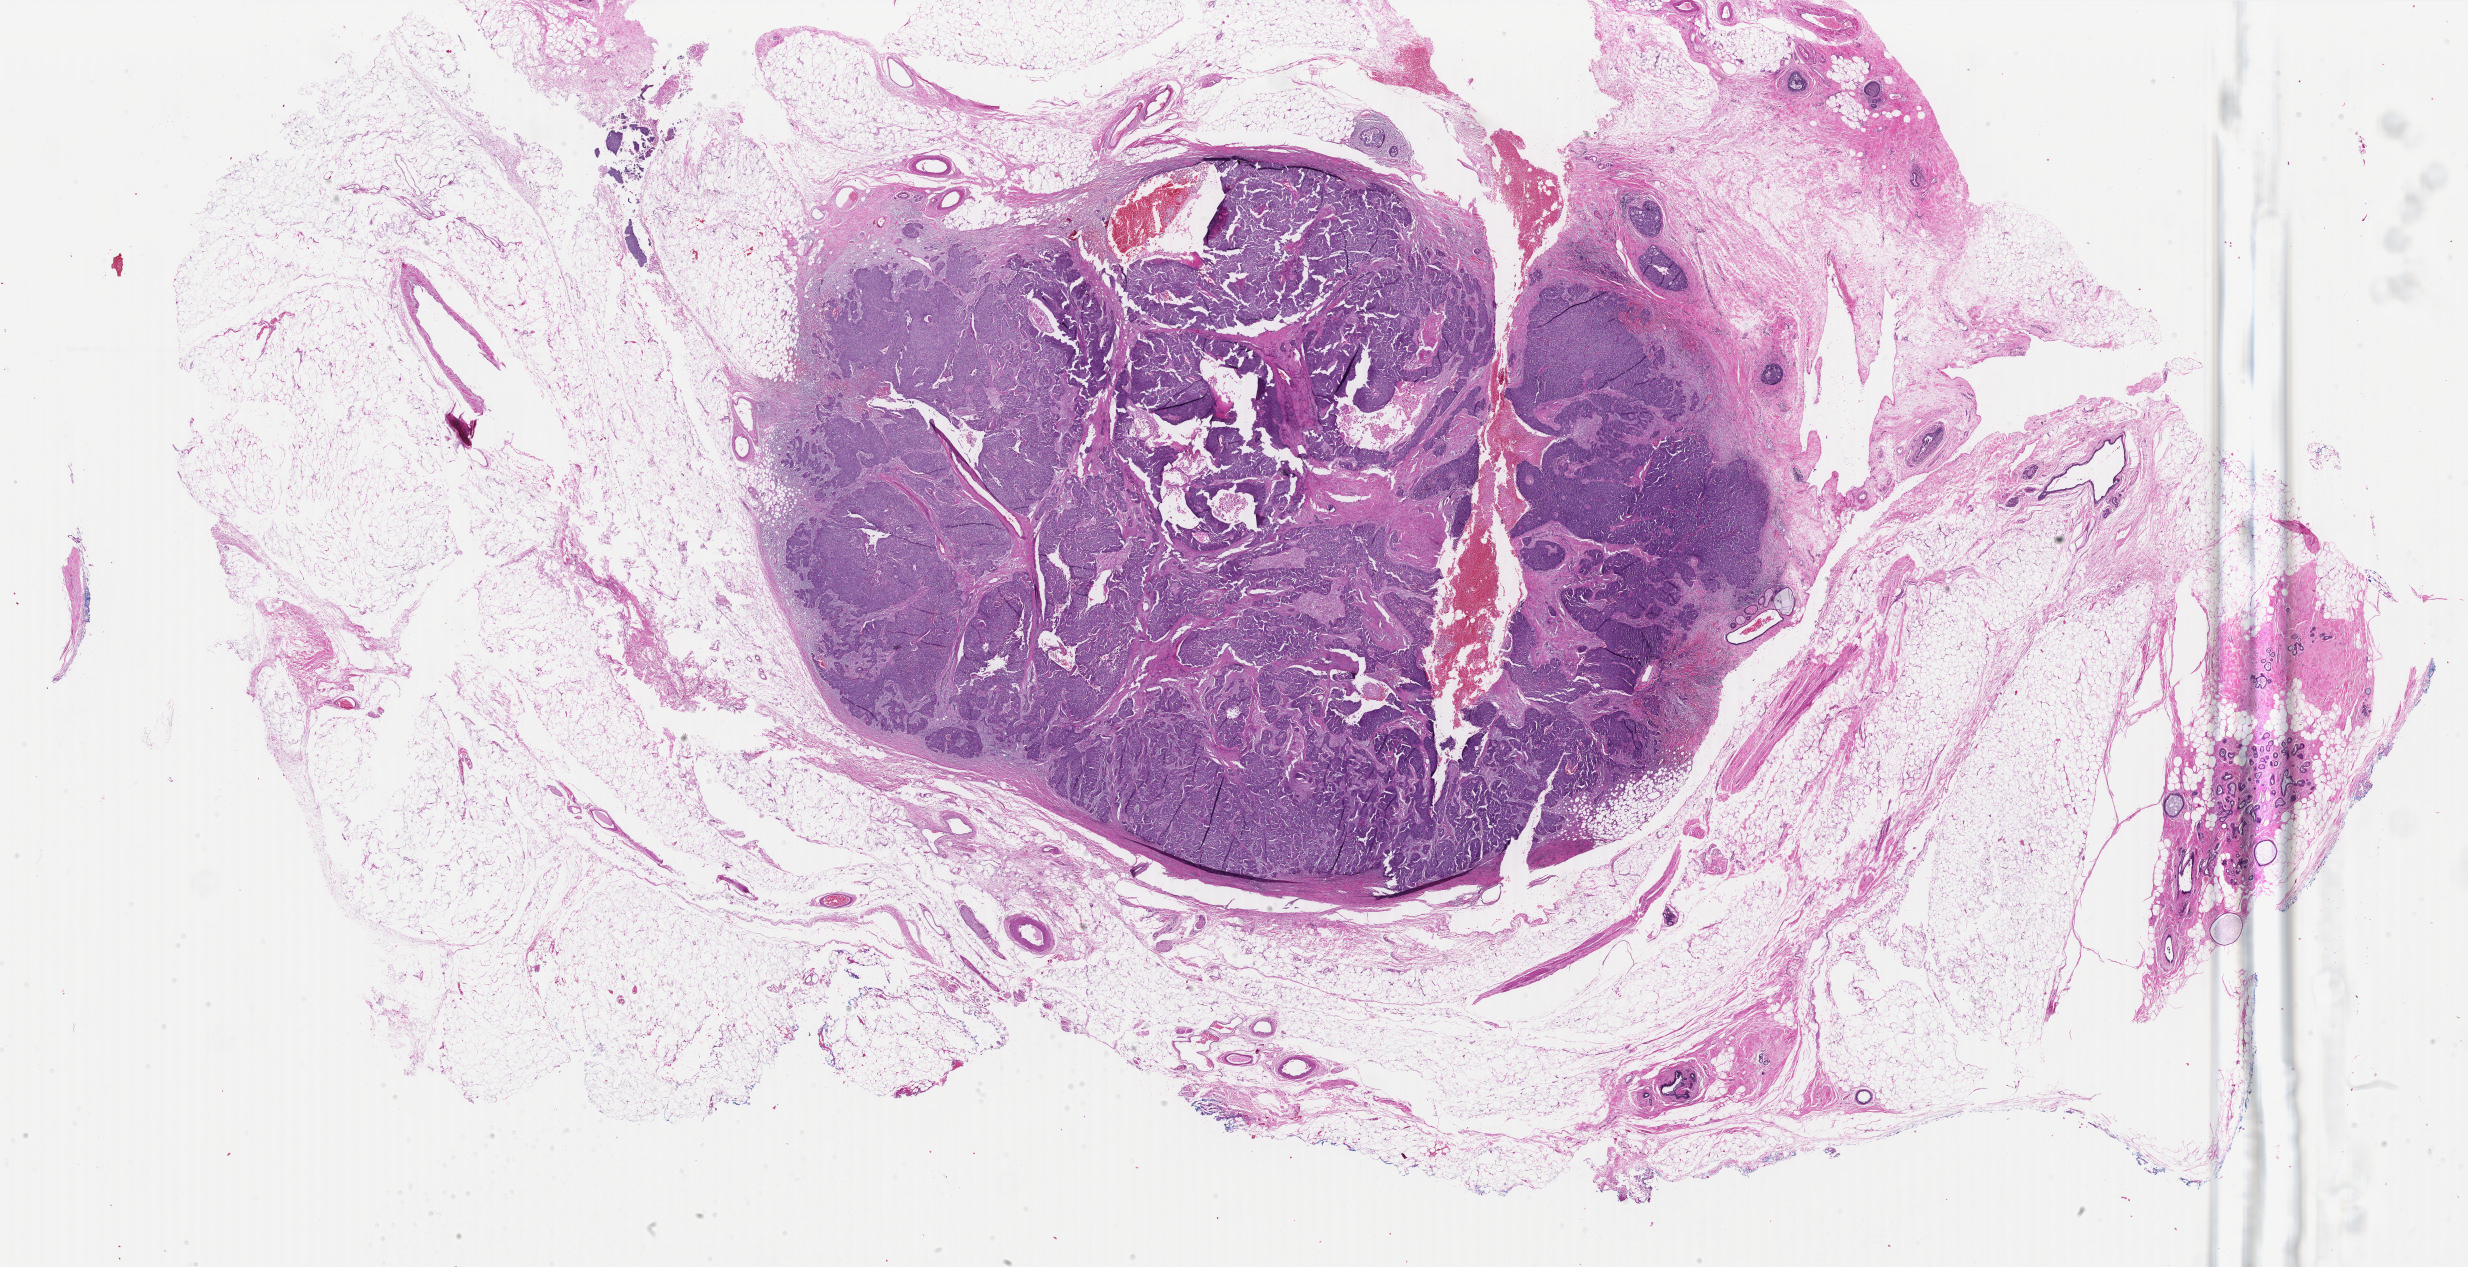
Whole-slide histology image, H&E, whole scanned area (about 39.3 x 20.2 mm, acquisition: 40x scan) shown as a low-resolution overview. FFPE section. Breast, primary tumour sample. Female, age 63 years at initial diagnosis.
• lymph nodes positive (case pathology): 1 of 22 examined
• laterality: left
• AJCC pathologic stage: IIB (6th edition)
• histologic diagnosis: Infiltrating duct carcinoma, NOS